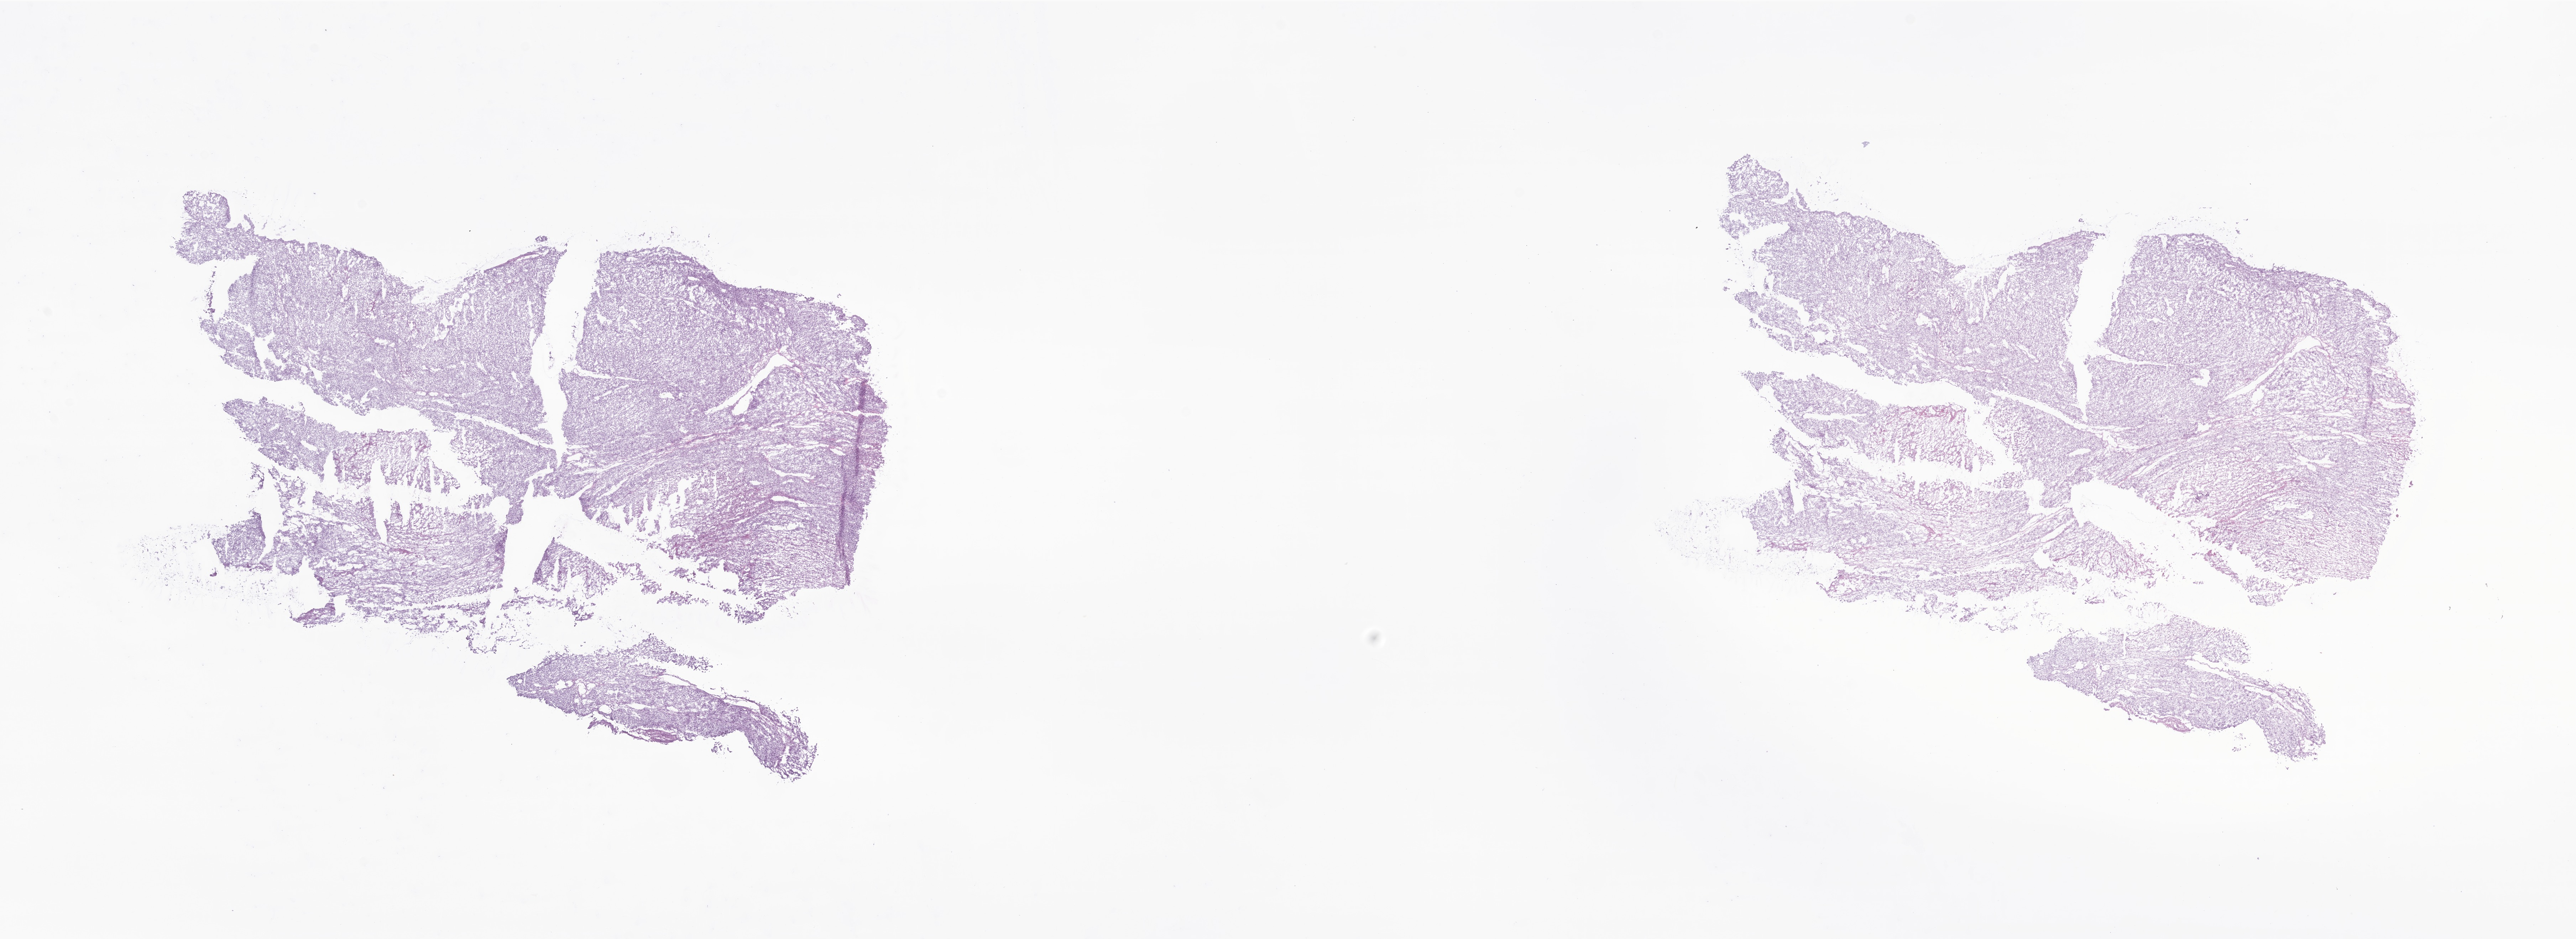
Whole-slide image, hematoxylin and eosin (H&E) stain of tumor tissue from the ovary — shown as a low-resolution overview of the whole scanned area (about 30.5 x 11.1 mm); frozen section (OCT-embedded). Patient: female, age 90 months.
Diagnosis (ICD-O-3 morphology term): Granulosa cell tumor, juvenile.